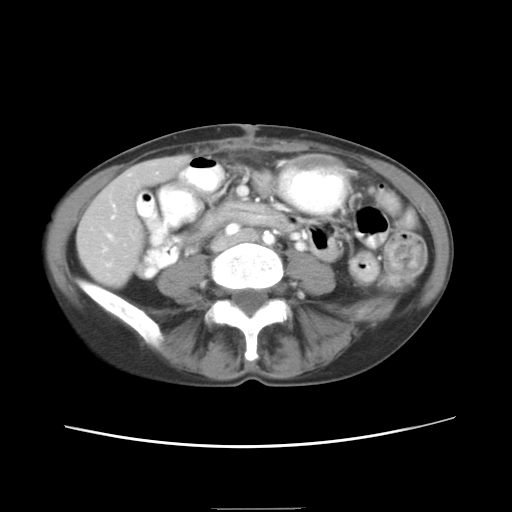
Contrast-enhanced abdominal CT, one axial slice; slice 1 of 26 in the series (ordered by position); 120 kVp; soft-tissue window (W 400 / L 40 HU); 512 × 512 image matrix, field of view 340 × 340 mm. Female patient, age 65 years. Case-level facts recorded for this patient, not image findings: diagnosis: colorectal cancer liver metastases, imaged before liver resection; multiple liver metastases: no; chemotherapy before resection: yes.
Structures marked on this image (outlined manually by an expert reader):
- liver: bounding box <78,158,188,287> (left, top, right, bottom; pixels)
- planned liver remnant (the part of the liver to remain after resection): <78,158,188,287>